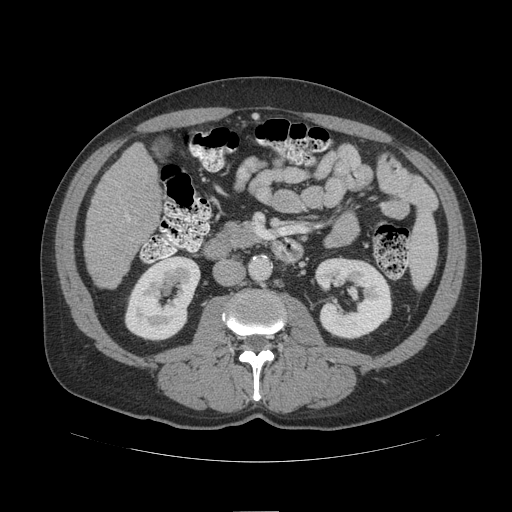
Contrast-enhanced abdominal CT (liver protocol), one axial slice; position 37 of 109 along the scan axis; 140 kVp; soft-tissue window (W 400 / L 40 HU); 512 × 512 image matrix. Case-level facts recorded for this patient, not image findings: diagnosis: hepatocellular carcinoma (patient treated with transarterial chemoembolisation; whether this scan precedes or follows treatment is not stated here); TNM stage (as recorded): Stage-IIIB.
Structures marked on this image (semi-automatic segmentation, software-assisted and operator-edited):
- liver parenchyma outside the tumour (the mass and vessels are separate outlines, so this box may not span the whole liver): bounding box [x1, y1, x2, y2] px = [84, 144, 160, 288]